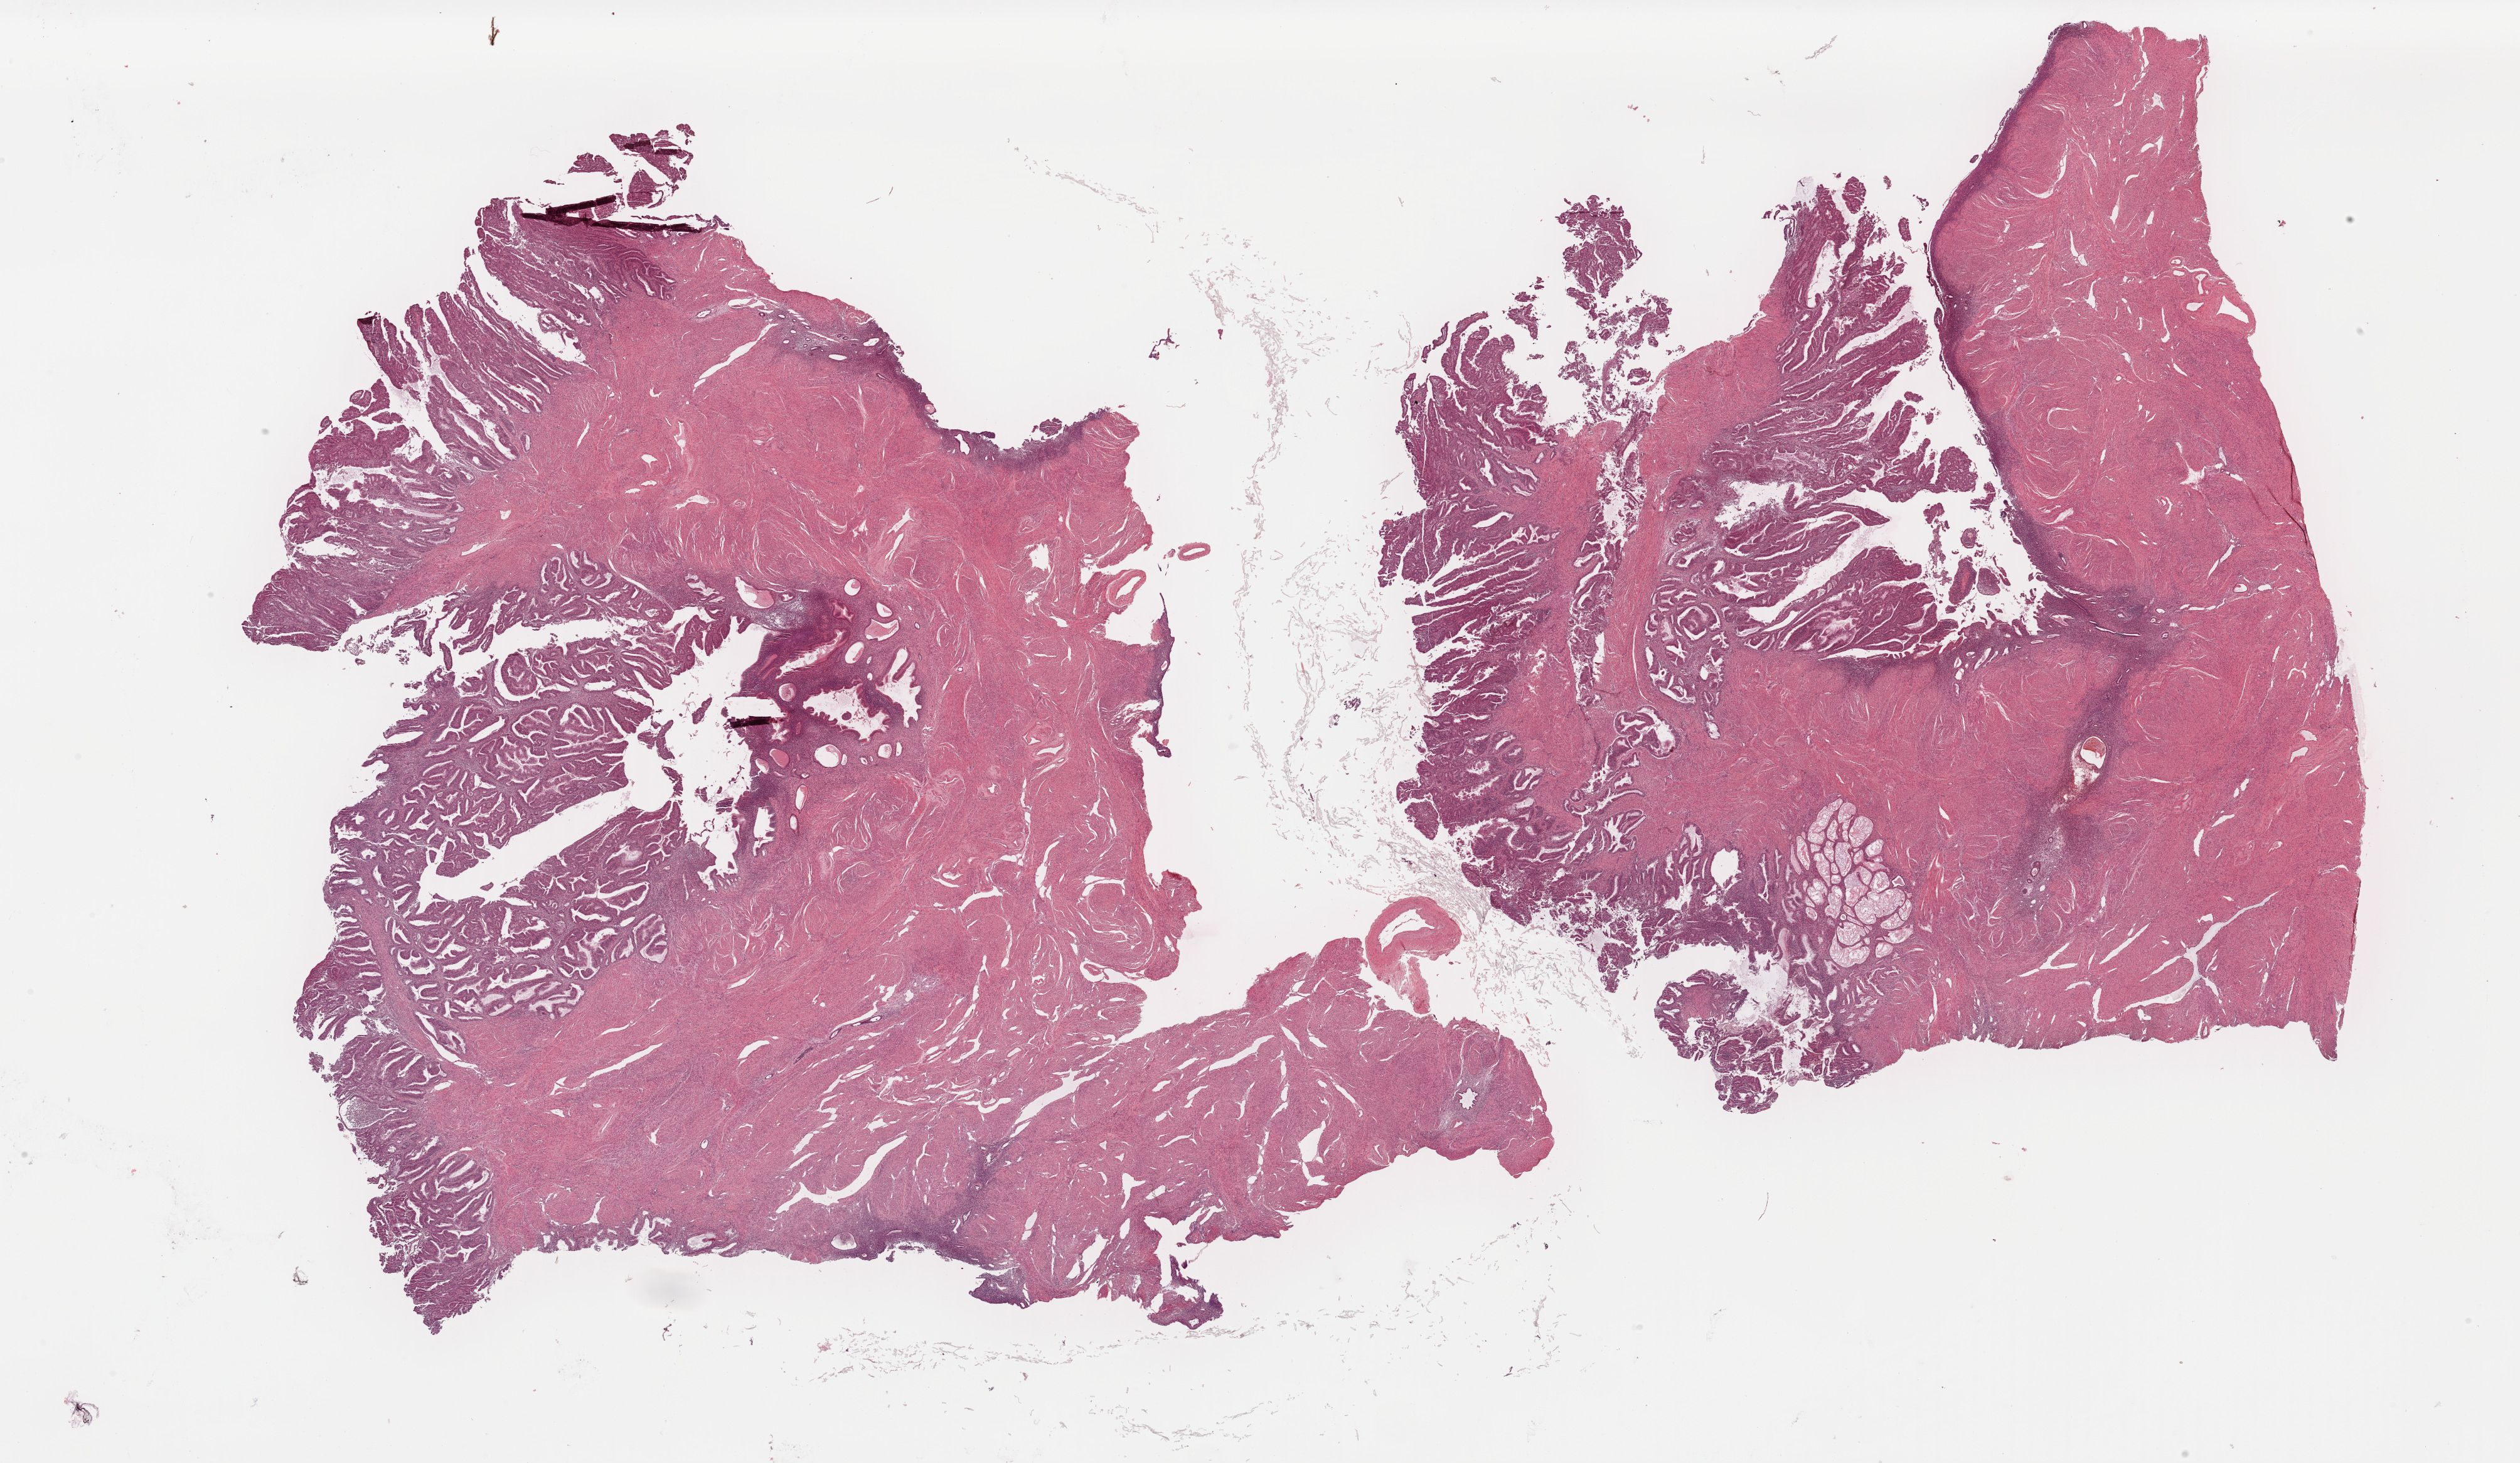
Whole-slide histology image, H&E, a low-resolution overview of the entire scanned area, about 31.7 x 18.4 mm; formalin-fixed paraffin-embedded (FFPE) diagnostic section; sample: primary tumour, uterus. Female, age 65 years at initial diagnosis. Histologic grade: G1 (well differentiated).
Pathologic diagnosis: Endometrioid adenocarcinoma, NOS (corpus uteri). FIGO stage: IB.